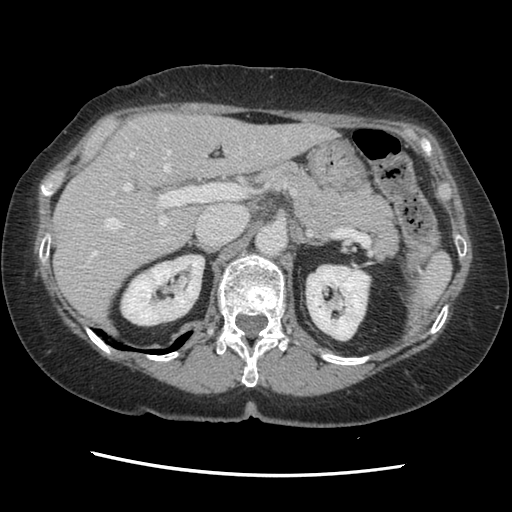
Contrast-enhanced abdominal CT, one axial slice. Slice 86 of 141 in the series (ordered by position). 120 kVp. Soft-tissue window (W 400 / L 40 HU). 2.5 mm slice thickness. 512 × 512 image matrix. Female patient, age 61 years. From the clinical record (not read from this slice): diagnosis: colorectal cancer liver metastases, imaged before liver resection; multiple liver metastases: no; largest metastasis: 2.4 cm; chemotherapy before resection: no.
Outlined on this slice (manually delineated by an expert):
- hepatic veins: bounding box (x1, y1, x2, y2) in pixels: (87, 129, 312, 266)
- liver: (55, 114, 332, 321)
- planned liver remnant (the part of the liver to remain after resection): (55, 113, 332, 321)
- portal vein (with intrahepatic branches): (111, 153, 241, 226)